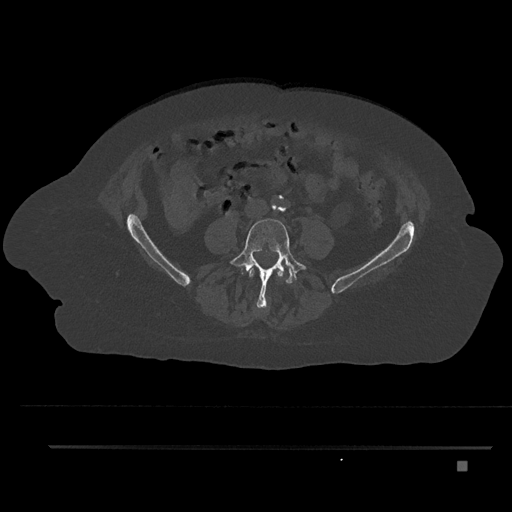
CT including the spine, one axial slice; position 82 of 797 along the scan axis; 120 kVp; bone window (W 1800 / L 400 HU); 512 × 512 image matrix. Patient: female, 76 years. From the clinical record (not read from this slice): primary cancer: lung.
Structures marked on this image (semi-automatically segmented with operator editing):
- L3 vertebra: bounding box (x1, y1, x2, y2) in pixels: (249, 268, 283, 278)
- L4 vertebra: (230, 218, 308, 311)
- L5 vertebra: (286, 266, 295, 284)